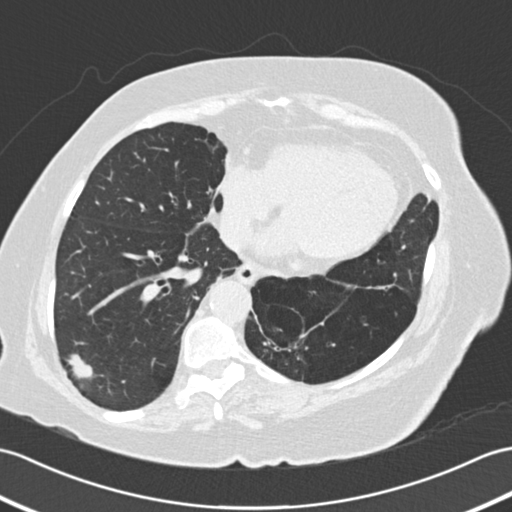
Low-dose screening chest CT, one axial slice; 120 kVp; lung window (W 1500 / L -600 HU); 2 mm slice thickness; 512 × 512 image matrix, field of view 353 × 353 mm.
Outlined on this slice (expert manual segmentation):
- lesion 1 (tumor, lower lobe of right lung): bounding box (x1, y1, x2, y2) in pixels: (67, 354, 93, 378)